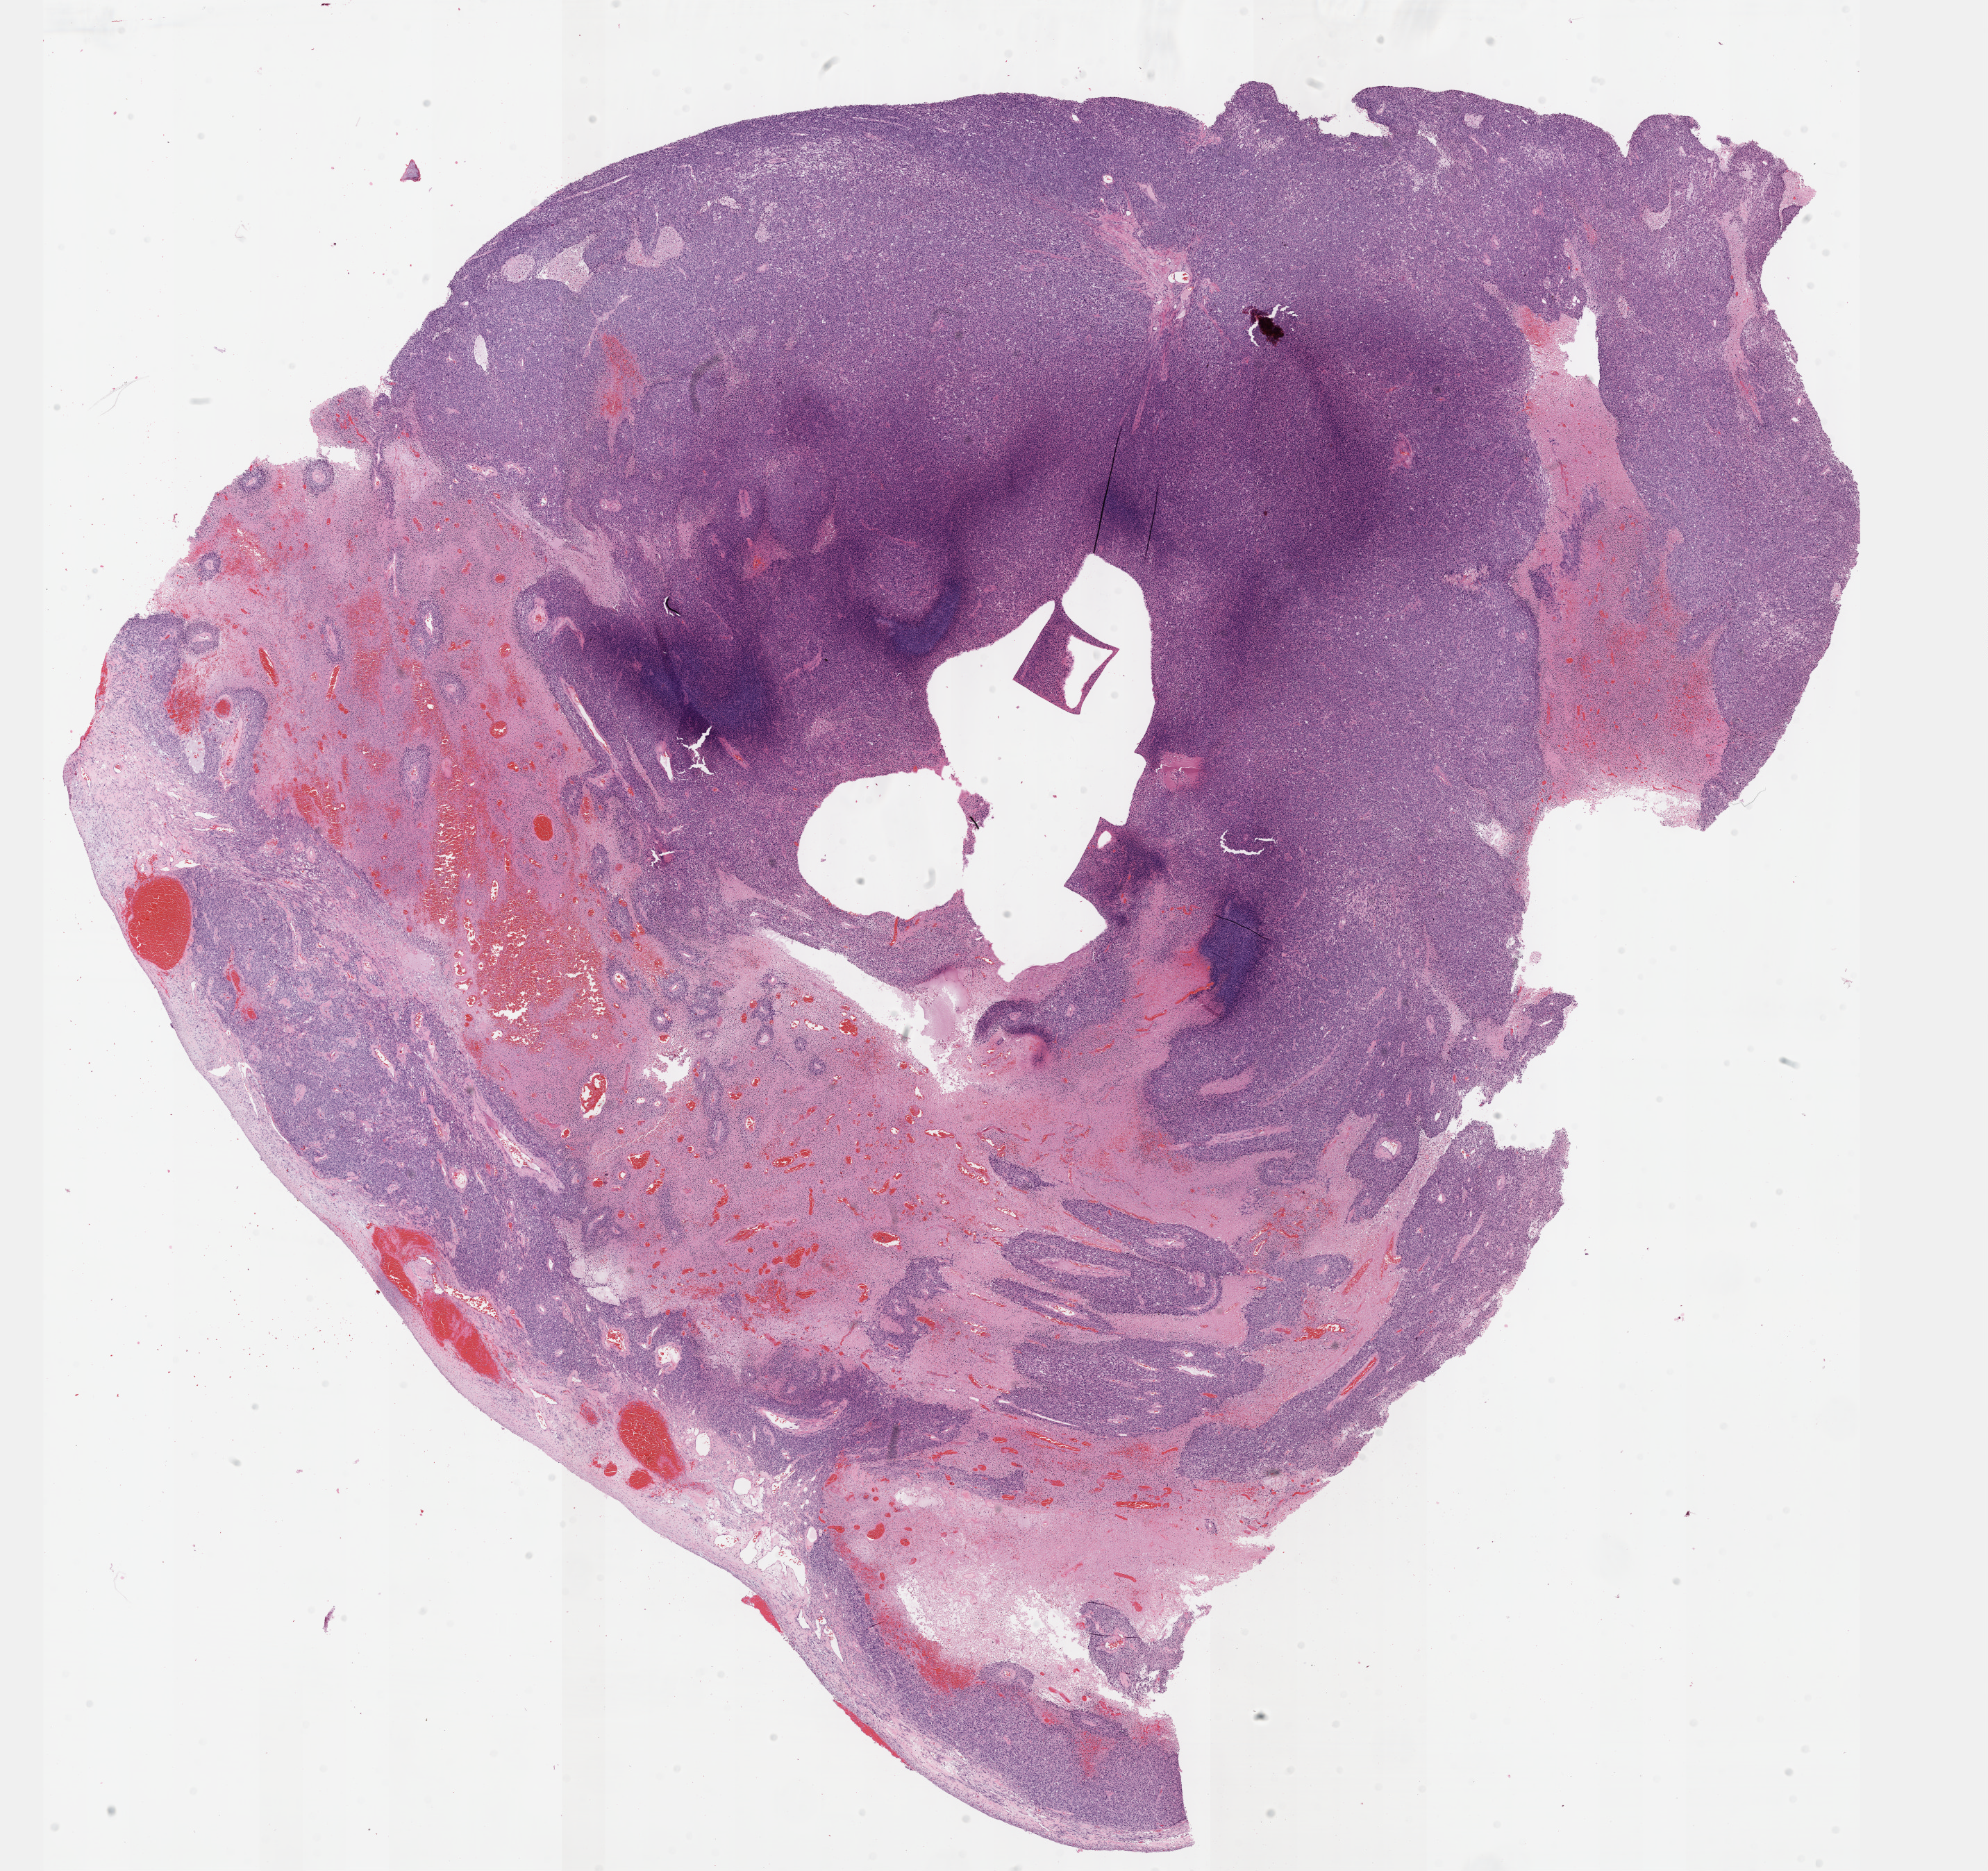
Whole-slide histology image, Hematoxylin and eosin (H&E) stained — whole scanned area (about 23.1 x 21.8 mm, slide scanned at 40x) shown as a low-resolution overview. Formalin-fixed paraffin-embedded (FFPE) diagnostic section. Primary tumour sample from the uterus. Patient: female, age at initial diagnosis 58 years.
• pathologic diagnosis: Leiomyosarcoma, NOS